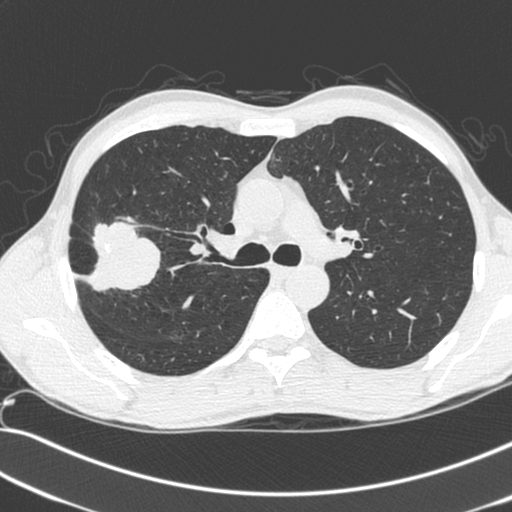
Axial slice from a low-dose chest CT screening exam; baseline screening round; lung window (W 1500 / L -600 HU); standard (soft-tissue) reconstruction kernel (C); slice 86 of 281 in the series; 512 × 512 image matrix. Male, age 55 years at enrolment. Current smoker at enrolment.
• Expert-annotated lung lesion, bounding box <68,224,154,300> (left, top, right, bottom; pixels).
• The exam's reader record, not a measurement of the box and not confirmed to be the same lesion: non-calcified nodule or mass ≥4 mm, right upper lobe, 52 × 39 mm, spiculated (stellate) margins, soft tissue attenuation.
• Official screen result: positive, change unspecified: nodule(s) >= 4 mm or enlarging nodule(s), mass(es), or other non-specific abnormalities suspicious for lung cancer.
• Later outcome: lung cancer diagnosed 25 days after this screen — large cell neuroendocrine carcinoma, right upper lobe, poorly differentiated (G3), stage IIB (AJCC 6th edition), 49 mm at pathology.